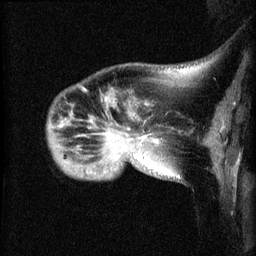
Breast MRI (dynamic contrast-enhanced), one sagittal slice. Position 12 of 60 along the scan axis. Dynamic contrast-enhanced series, image 2 of 3 at this slice position (ordered by acquisition). 1.5 T. TE 4.2 ms, TR 8.2 ms. 2.1 mm slice thickness. 256 × 256 image matrix. Patient: female, 50 years.
Structures marked on this image (semi-automatically segmented with operator editing):
- analysis volume of interest (the breast-tissue region the enhancement analysis was run in; not a lesion): bounding box (x1, y1, x2, y2) in pixels: (47, 94, 169, 180)
- tumour enhancement mask (voxels above the 70 % enhancement threshold inside the analysis volume of interest): (116, 139, 159, 160)